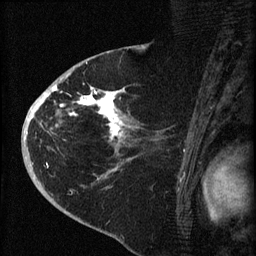
Breast MRI (dynamic contrast-enhanced), one sagittal slice. Dynamic contrast-enhanced series, image 2 of 4 at this slice position (ordered by acquisition). 1.5 T. TE 4.2 ms, TR 8.2 ms. 256 × 256 image matrix. Patient: female, 71 years.
Outlined on this slice (semi-automatic segmentation, software-assisted and operator-edited):
- analysis volume of interest (the breast-tissue region the enhancement analysis was run in; not a lesion): bounding box [x1, y1, x2, y2] px = [35, 75, 153, 190]
- tumour enhancement mask (voxels above the 70 % enhancement threshold inside the analysis volume of interest): [36, 75, 132, 142]